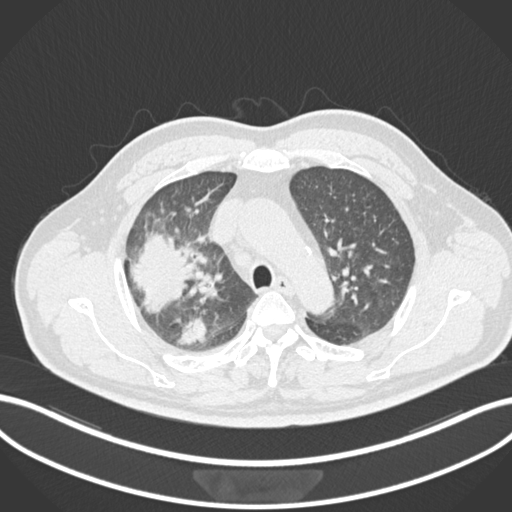
Chest CT, one axial slice. Position 669 of 852 along the scan axis. Reconstruction kernel B30f. Lung window (W 1500 / L -600 HU). 1 mm slice thickness. 512 × 512 image matrix, field of view 400 × 400 mm. Patient: male, 55 years. Case-level facts recorded for this patient, not image findings: clinical TNM (as recorded): T3 N2 M1.
Structures marked on this image (rectangle marked by the reading radiologist):
- lung tumour (recorded histology: adenocarcinoma): box from (x=128, y=225) to (x=195, y=313) px